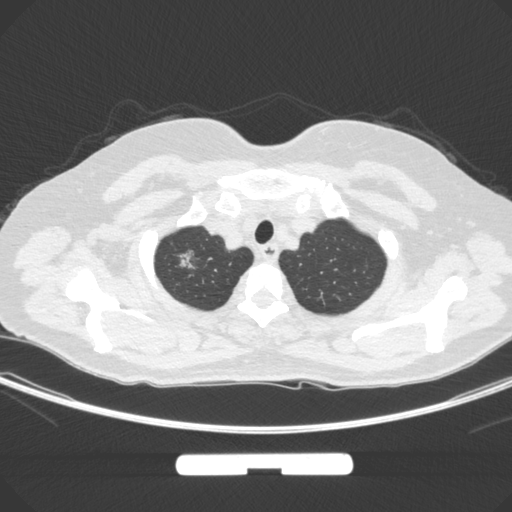
Chest CT, one axial slice; position 261 of 295 along the scan axis; lung window (W 1500 / L -600 HU); 1 mm slice thickness; 512 × 512 image matrix, field of view 369 × 369 mm. Female patient, age 58 years. From the clinical record (not read from this slice): clinical TNM (as recorded): T1b N0 M0; histopathological grade: G2-3.
Structures marked on this image (bounding box drawn by a radiologist):
- lung tumour (recorded histology: adenocarcinoma): box from (x=169, y=239) to (x=200, y=279) px